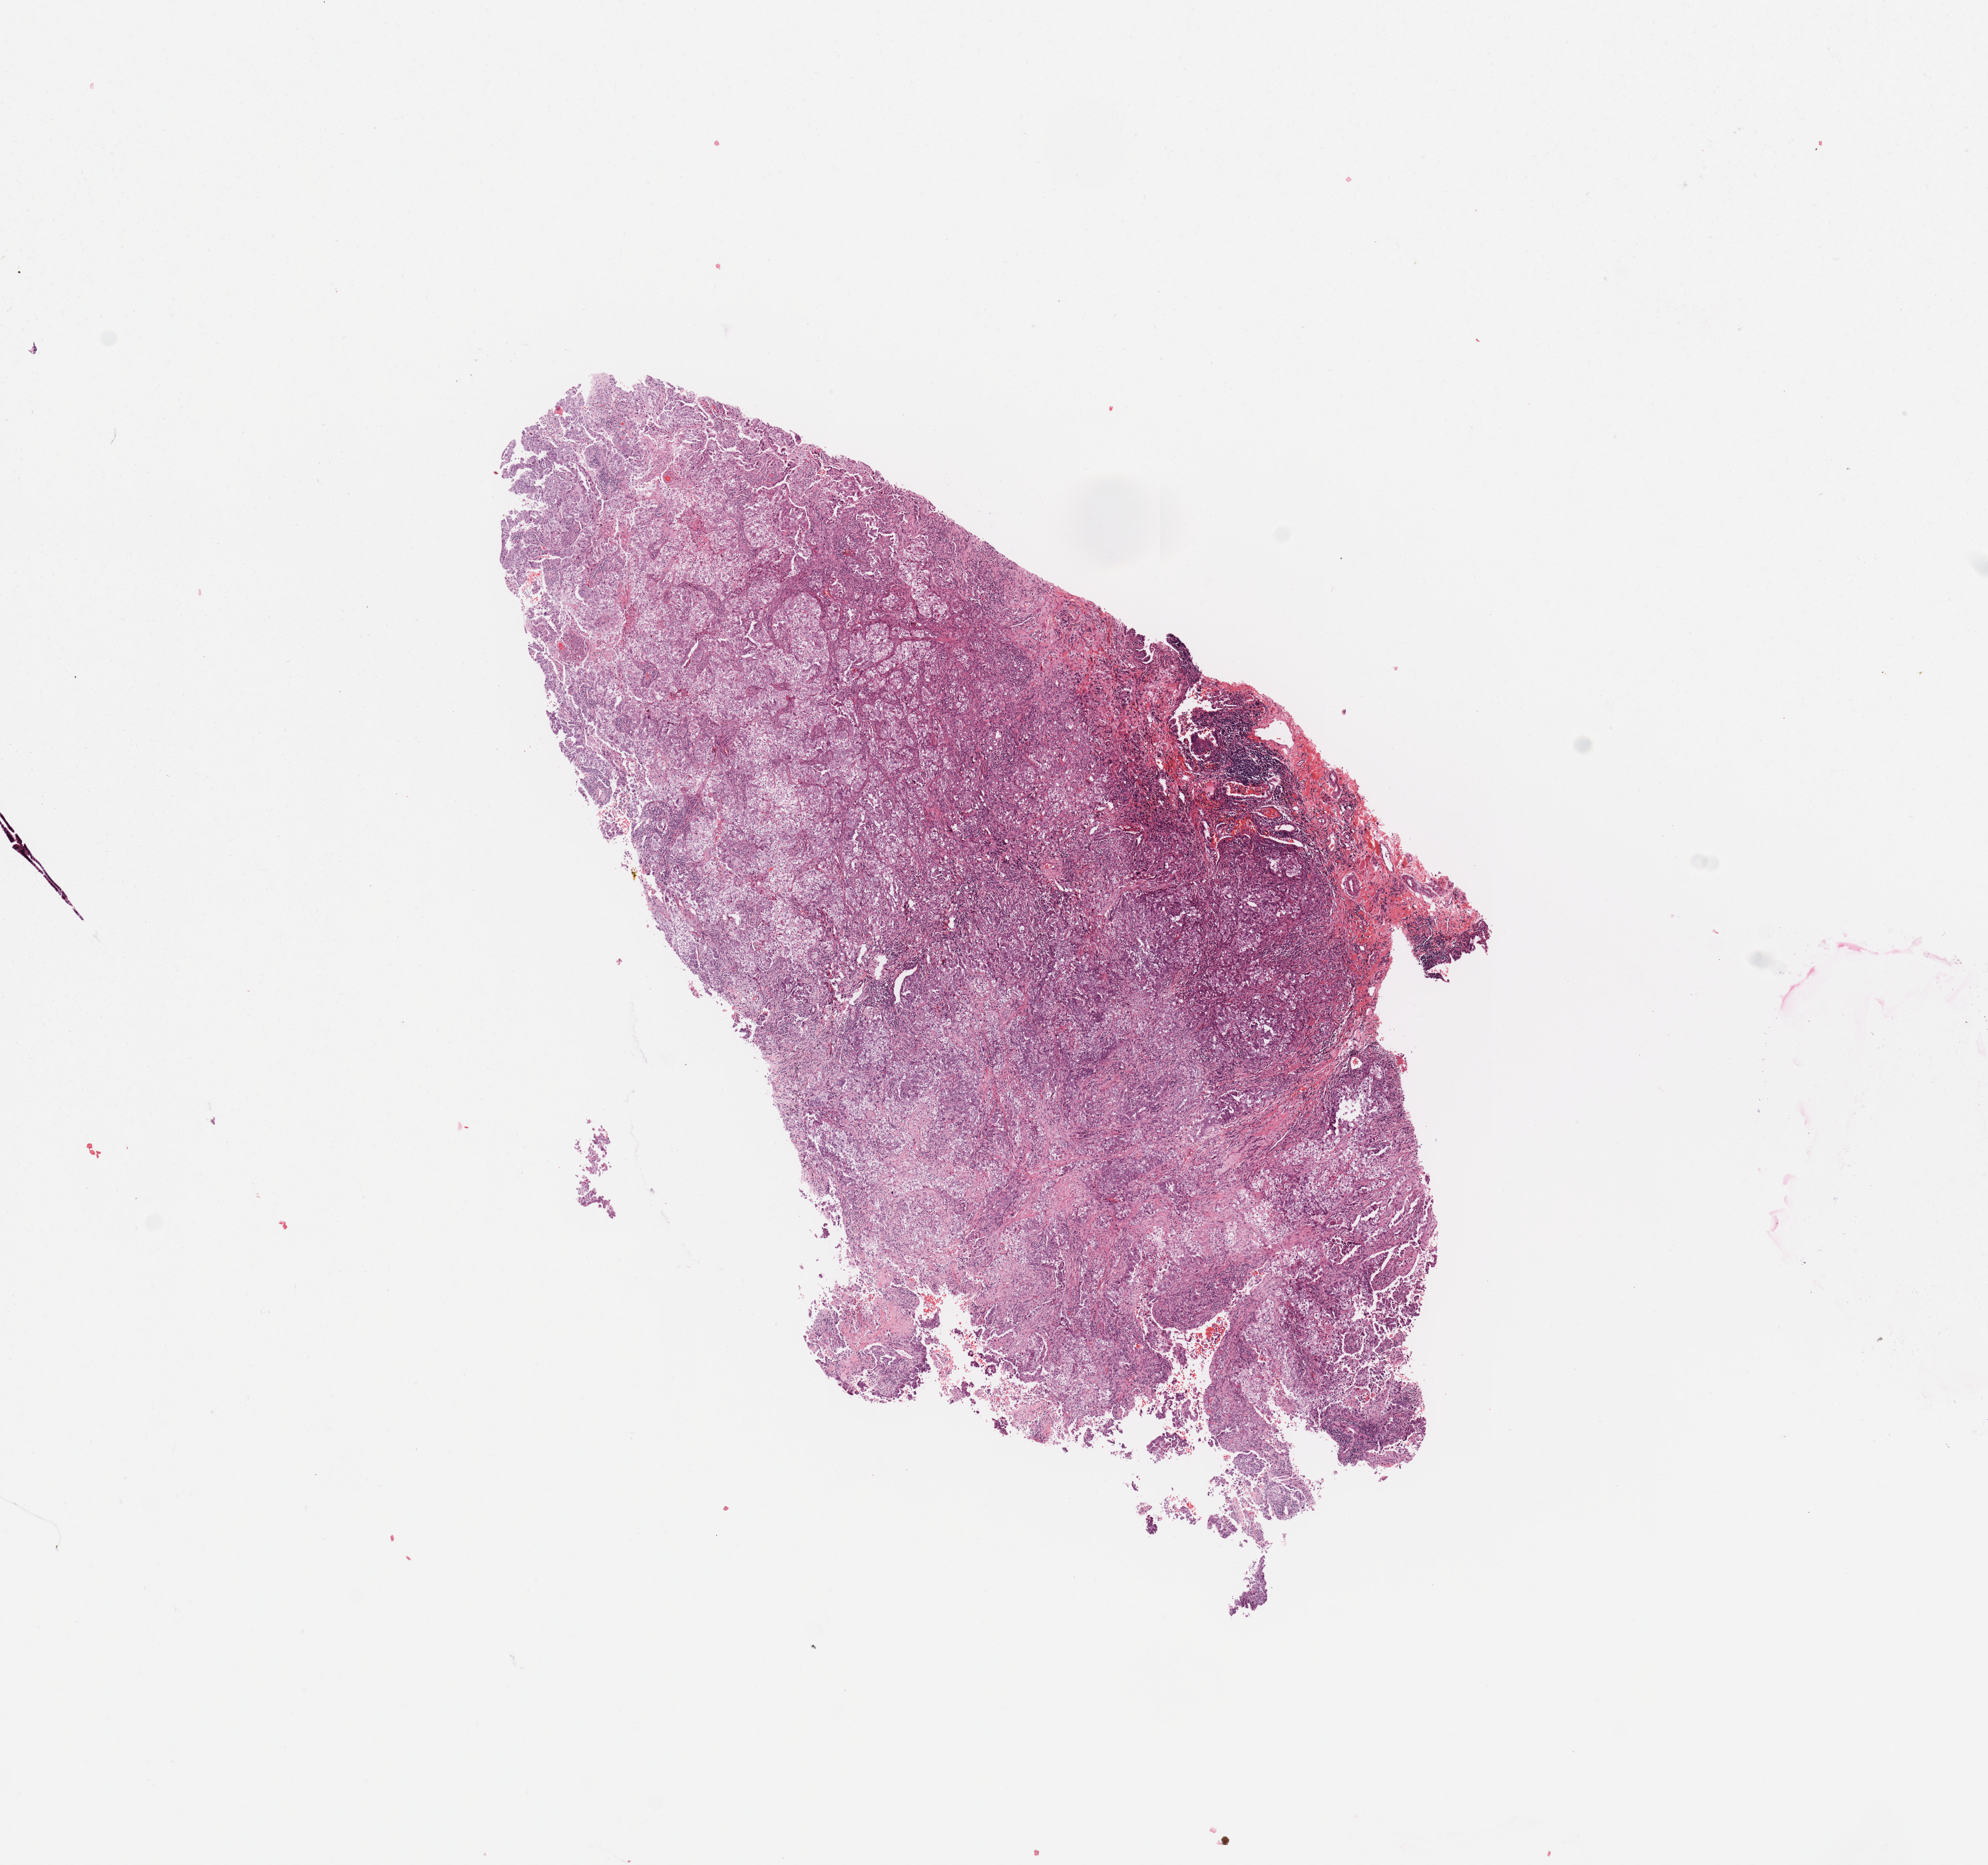
Hematoxylin and eosin (H&E) stained whole-slide image — low-resolution overview of the scanned area, about 11.8 x 11.1 mm; tumour tissue sample, sampled site: lung. Patient: male, age 70 years. Histologic grade: G3 (poorly differentiated). Slide review estimates, as recorded: tumour nuclei 70%, necrosis 5%.
* primary tumour site (as recorded): left upper lobe
* AJCC pathologic stage: IA
* diagnosis: Adenocarcinoma, NOS